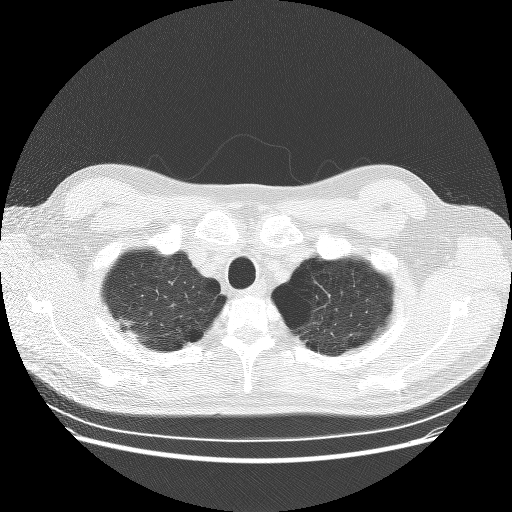
Low-dose screening chest CT, one axial slice; slice 234 of 253 in the series (ordered by position); 120 kVp; lung window (W 1500 / L -600 HU); 2.5 mm slice thickness; 512 × 512 image matrix, field of view 370 × 370 mm.
Annotated regions visible in this slice (manually delineated by an expert):
- lesion 1 (tumor, upper lobe of right lung): bounding box <130,333,137,337> (left, top, right, bottom; pixels)